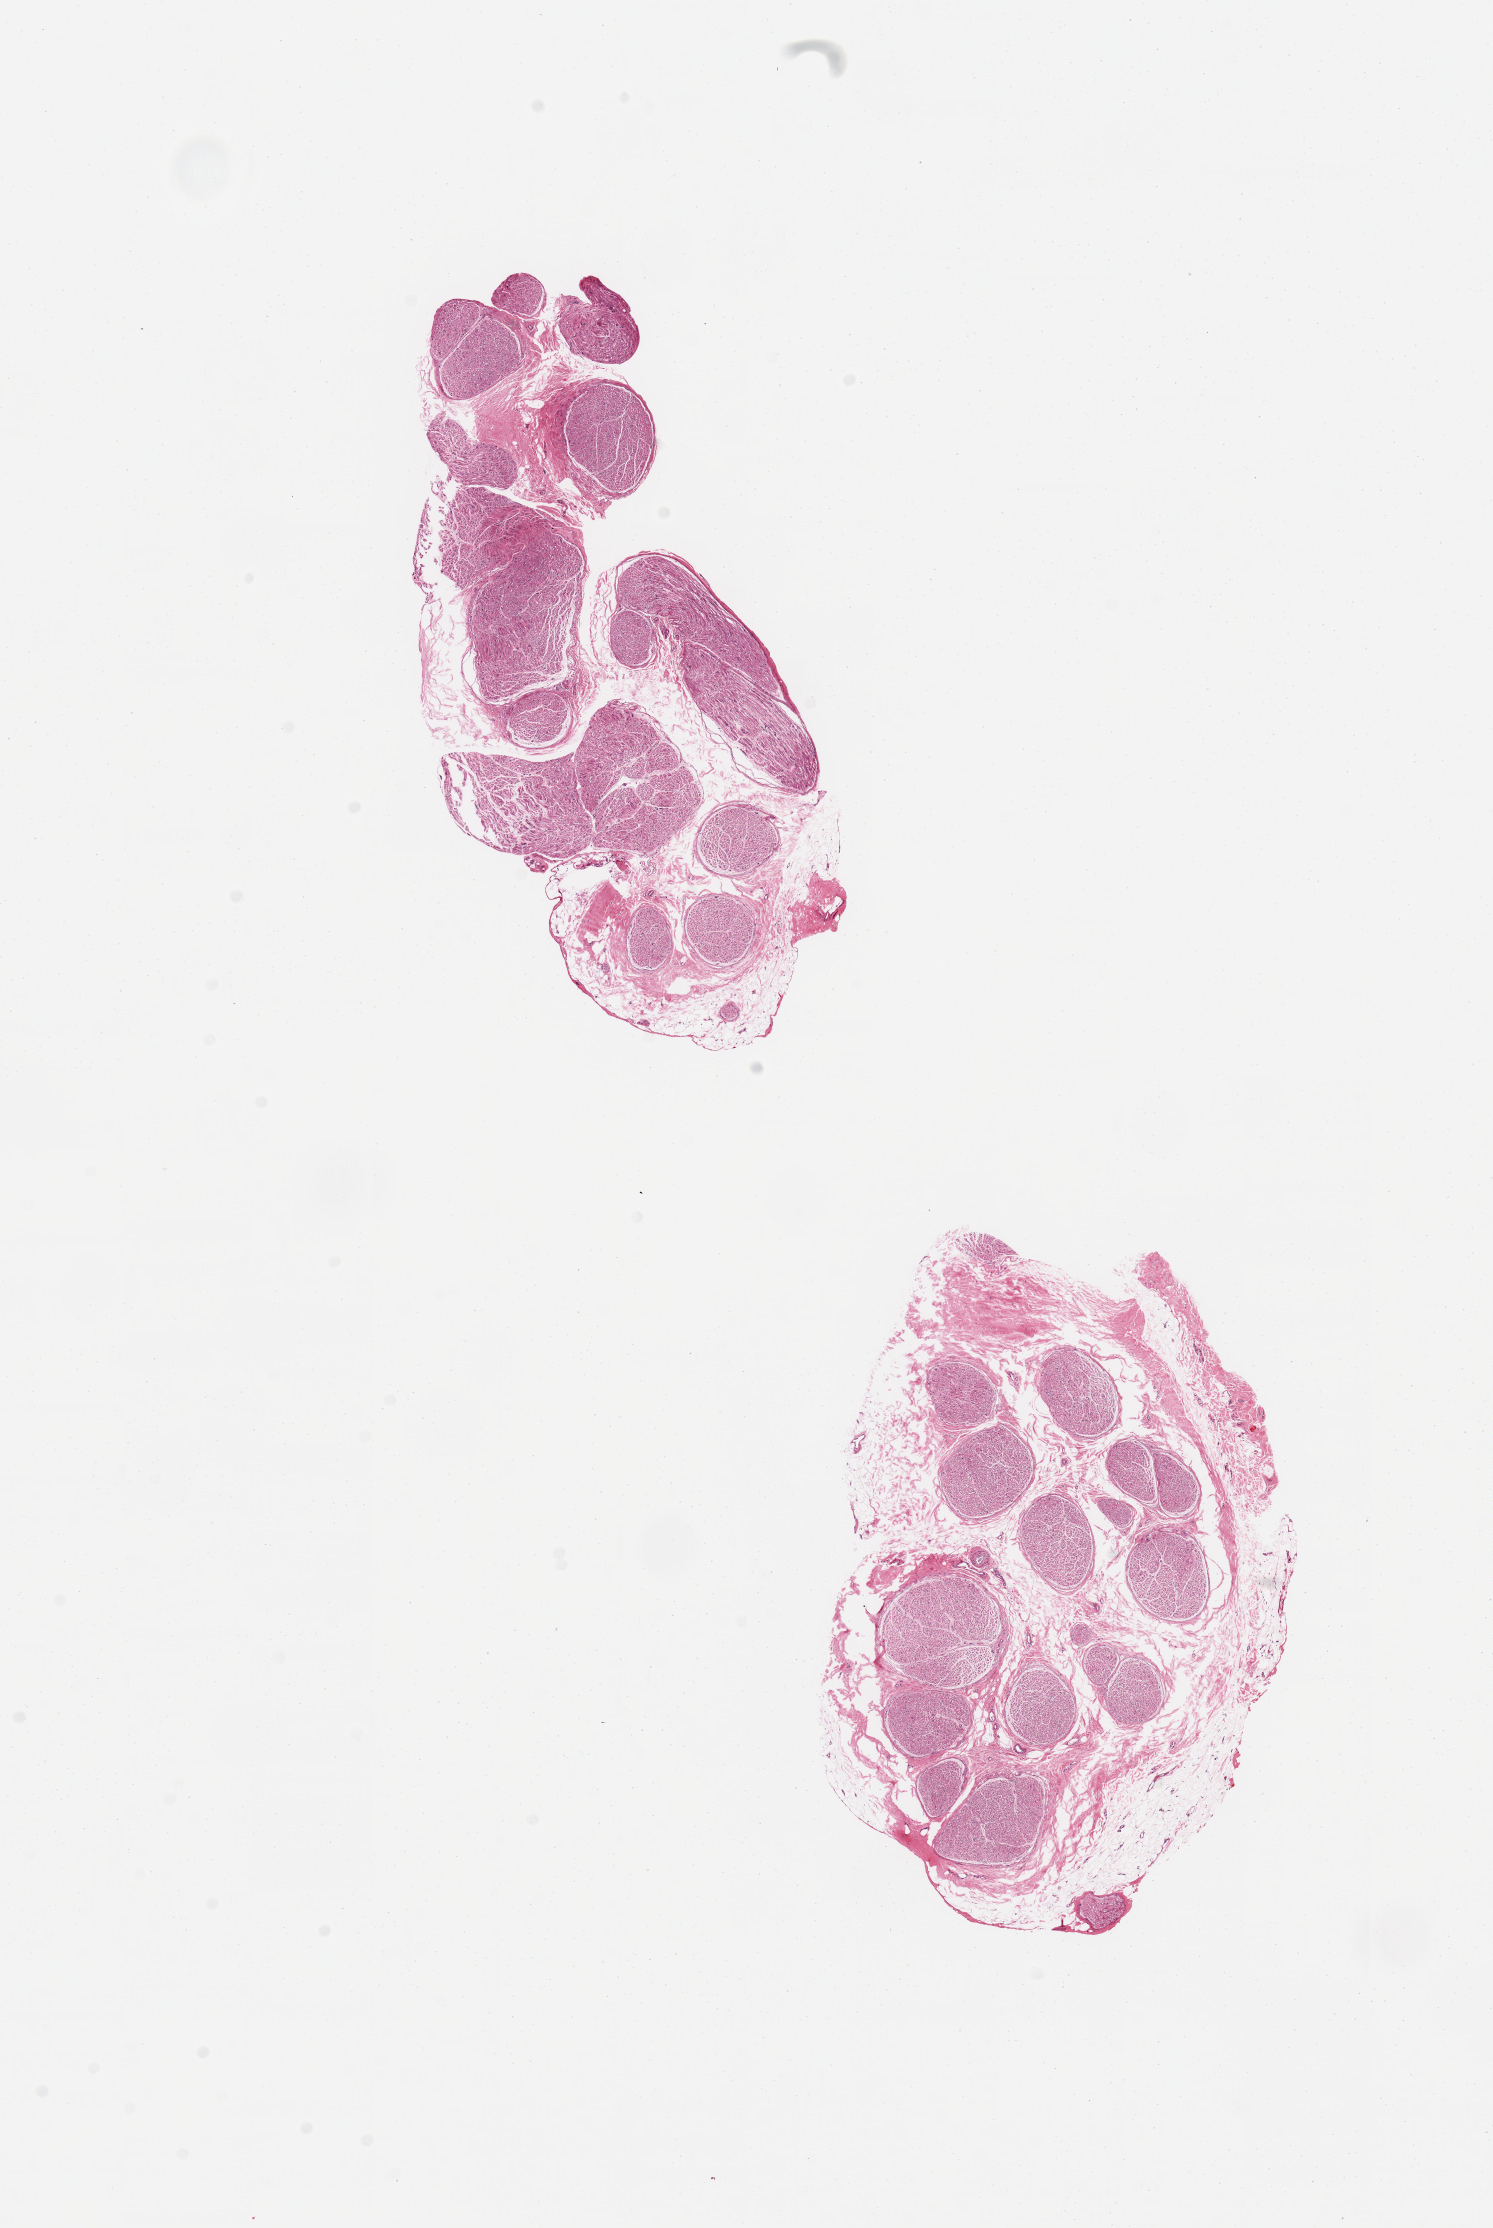
Whole-slide image, H&E stain, low-resolution overview of the scanned area, about 11.8 x 17.6 mm, PAXgene-fixed, paraffin-embedded tissue, sampled site (target tissue): tibial nerve, donor tissue sample. Female donor.
• reviewer comment on this tissue sample: 2 pieces; 30% and 40% internal/external fat